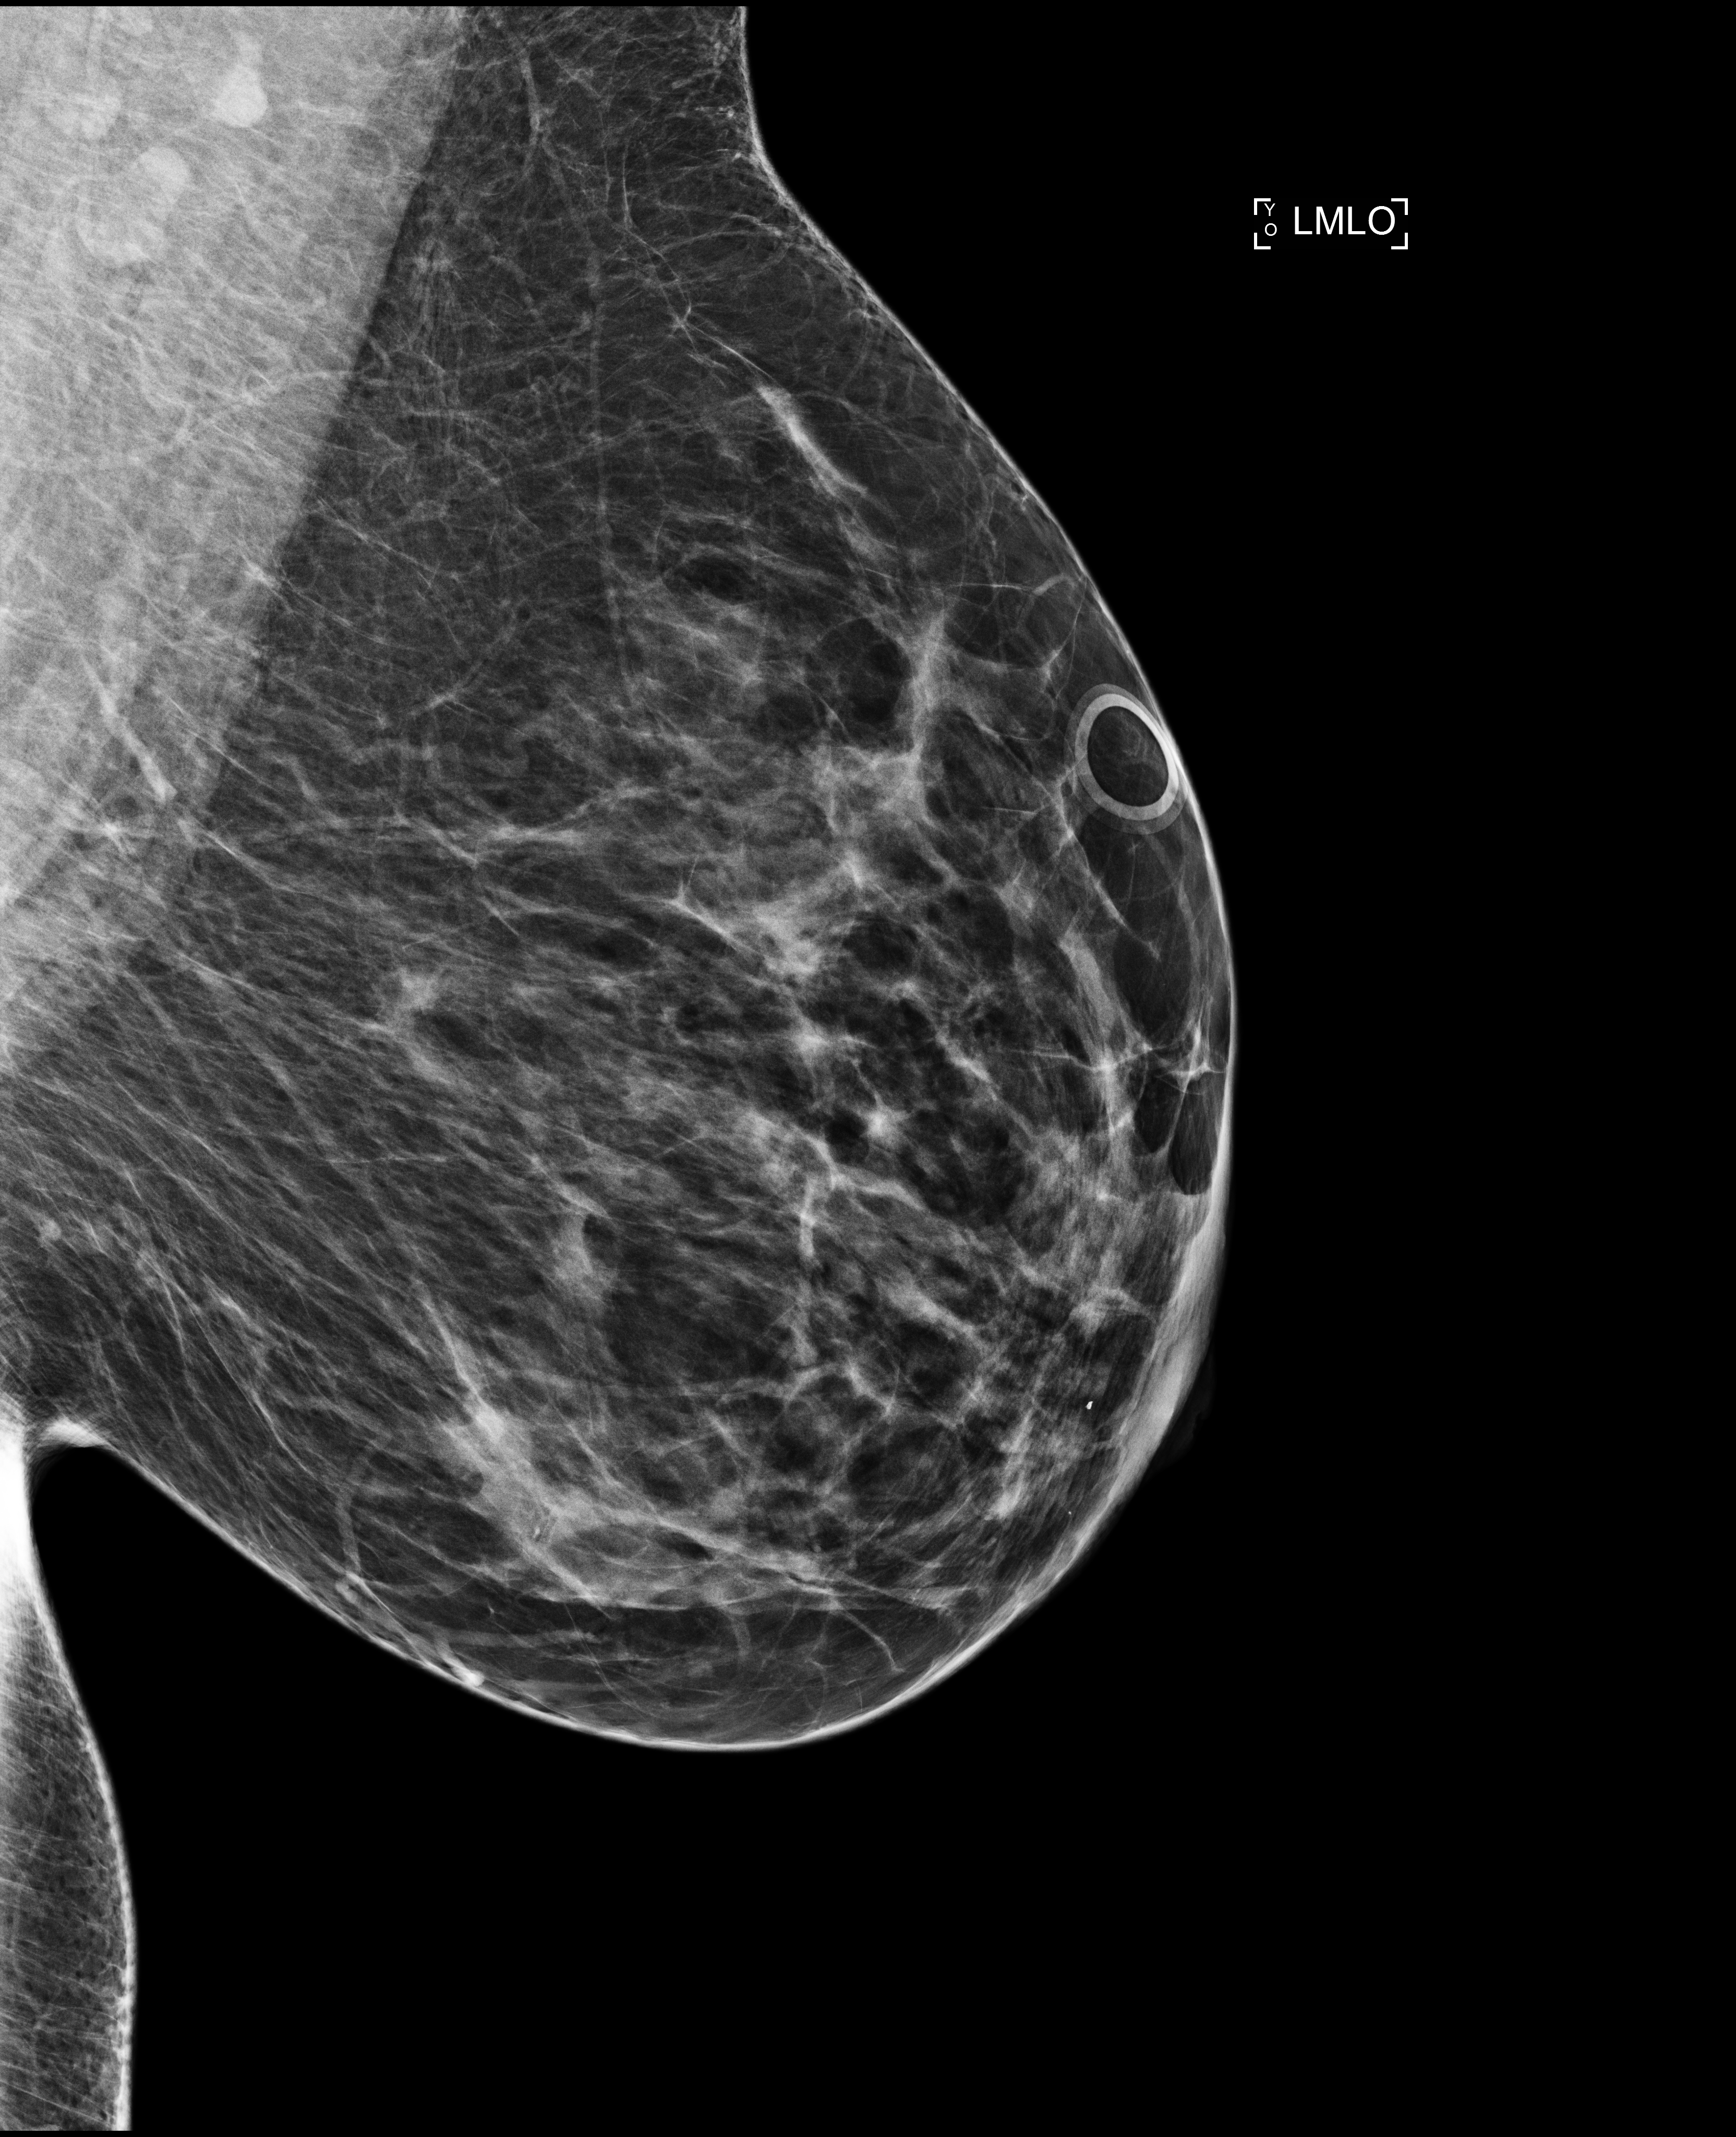
Full-field digital mammogram (FFDM); left breast; mediolateral oblique (MLO) view; annual screening mammography examination. Patient aged 46 years (female).
BI-RADS breast density category at the screening exam (both breasts, scale 1–4): 3. Final BI-RADS assessment for this screening round (tomosynthesis exam, both breasts): category 2. Recall: recalled for additional imaging after this screen.